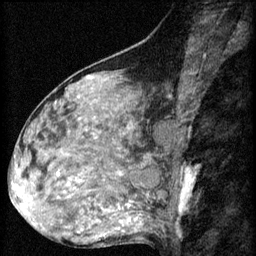
Breast MRI (dynamic contrast-enhanced), one sagittal slice; position 32 of 60 along the scan axis; 3 images stored at this slice position (order not interpretable as contrast timing); 1.5 T; TE 4.2 ms, TR 8.2 ms; 2 mm slice thickness; 256 × 256 image matrix. Patient: female, 48 years.
Outlined on this slice (semi-automatic segmentation, software-assisted and operator-edited):
- analysis volume of interest (the breast-tissue region the enhancement analysis was run in; not a lesion): bounding box <48,160,125,217> (left, top, right, bottom; pixels)
- tumour enhancement mask (voxels above the 70 % enhancement threshold inside the analysis volume of interest): <57,174,120,209>